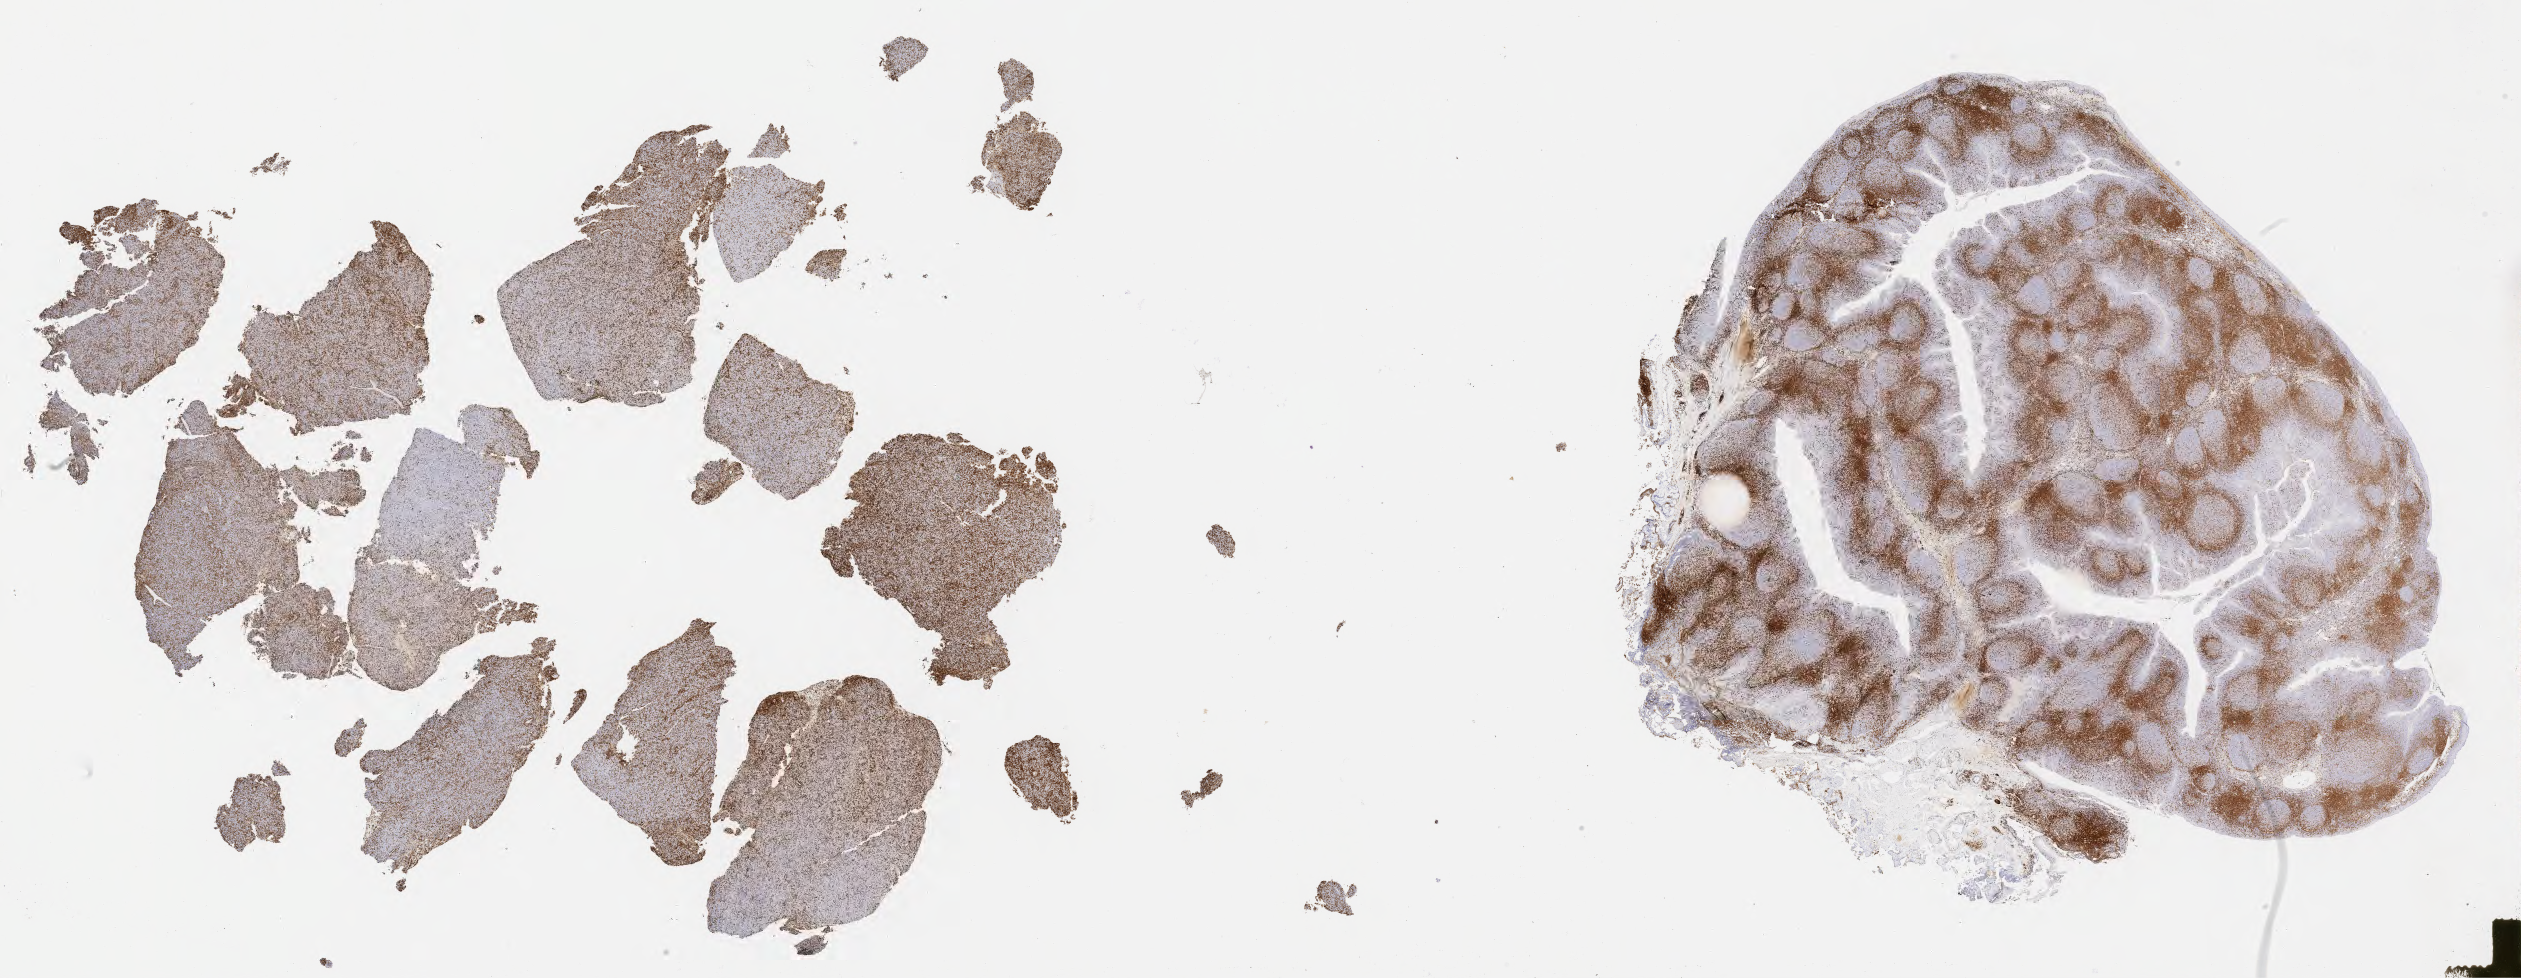
Whole-slide image, immunohistochemical stain for CD3 — low-resolution overview of the scanned area, about 40.7 x 15.8 mm, specimen: tumor tissue, anatomic site: lymph node. Female patient, aged 50.
Diagnosis: Diffuse large B-cell lymphoma, NOS.